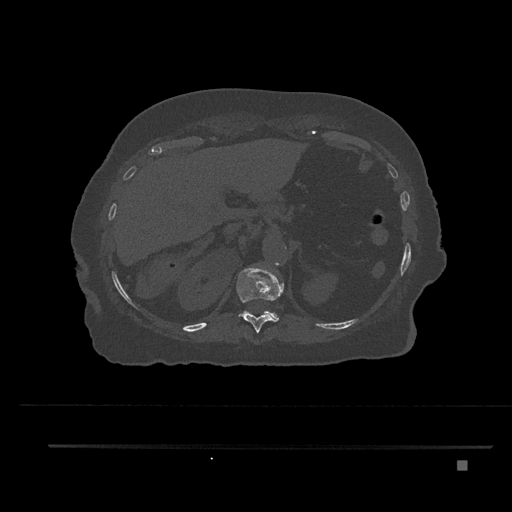
CT including the spine, one axial slice. Position 302 of 797 along the scan axis. Reconstruction kernel Br40s/3. Bone window (W 1800 / L 400 HU). 512 × 512 image matrix, field of view 437 × 437 mm. Female patient, age 76 years. Case-level facts recorded for this patient, not image findings: primary cancer: lung; vertebrae with lytic lesions (as recorded): T11, L3.
Structures marked on this image (semi-automatically segmented with operator editing):
- T11 vertebra: box from (x=236, y=266) to (x=284, y=333) px
- T12 vertebra: (x=240, y=311)–(x=279, y=321)